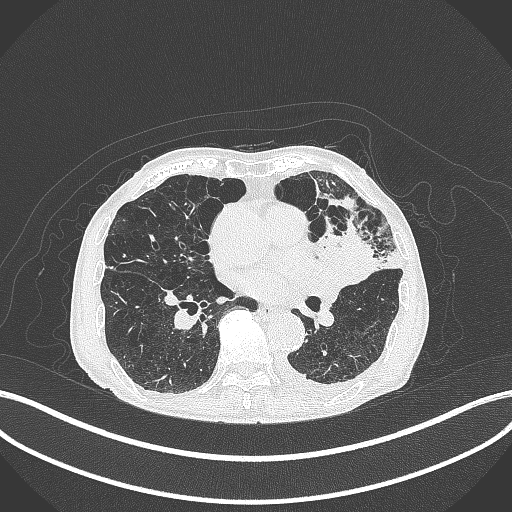
Chest CT, one axial slice. Slice 179 of 385 in the series (ordered by position). Reconstruction kernel B70f. Lung window (W 1500 / L -600 HU). 512 × 512 image matrix, field of view 400 × 400 mm. Patient: male, 90 years or older. Case-level facts recorded for this patient, not image findings: clinical TNM (as recorded): T2b N1 M0.
Outlined on this slice (bounding box drawn by a radiologist):
- lung tumour (recorded histology: squamous cell carcinoma): bounding box [x1, y1, x2, y2] px = [319, 227, 380, 287]